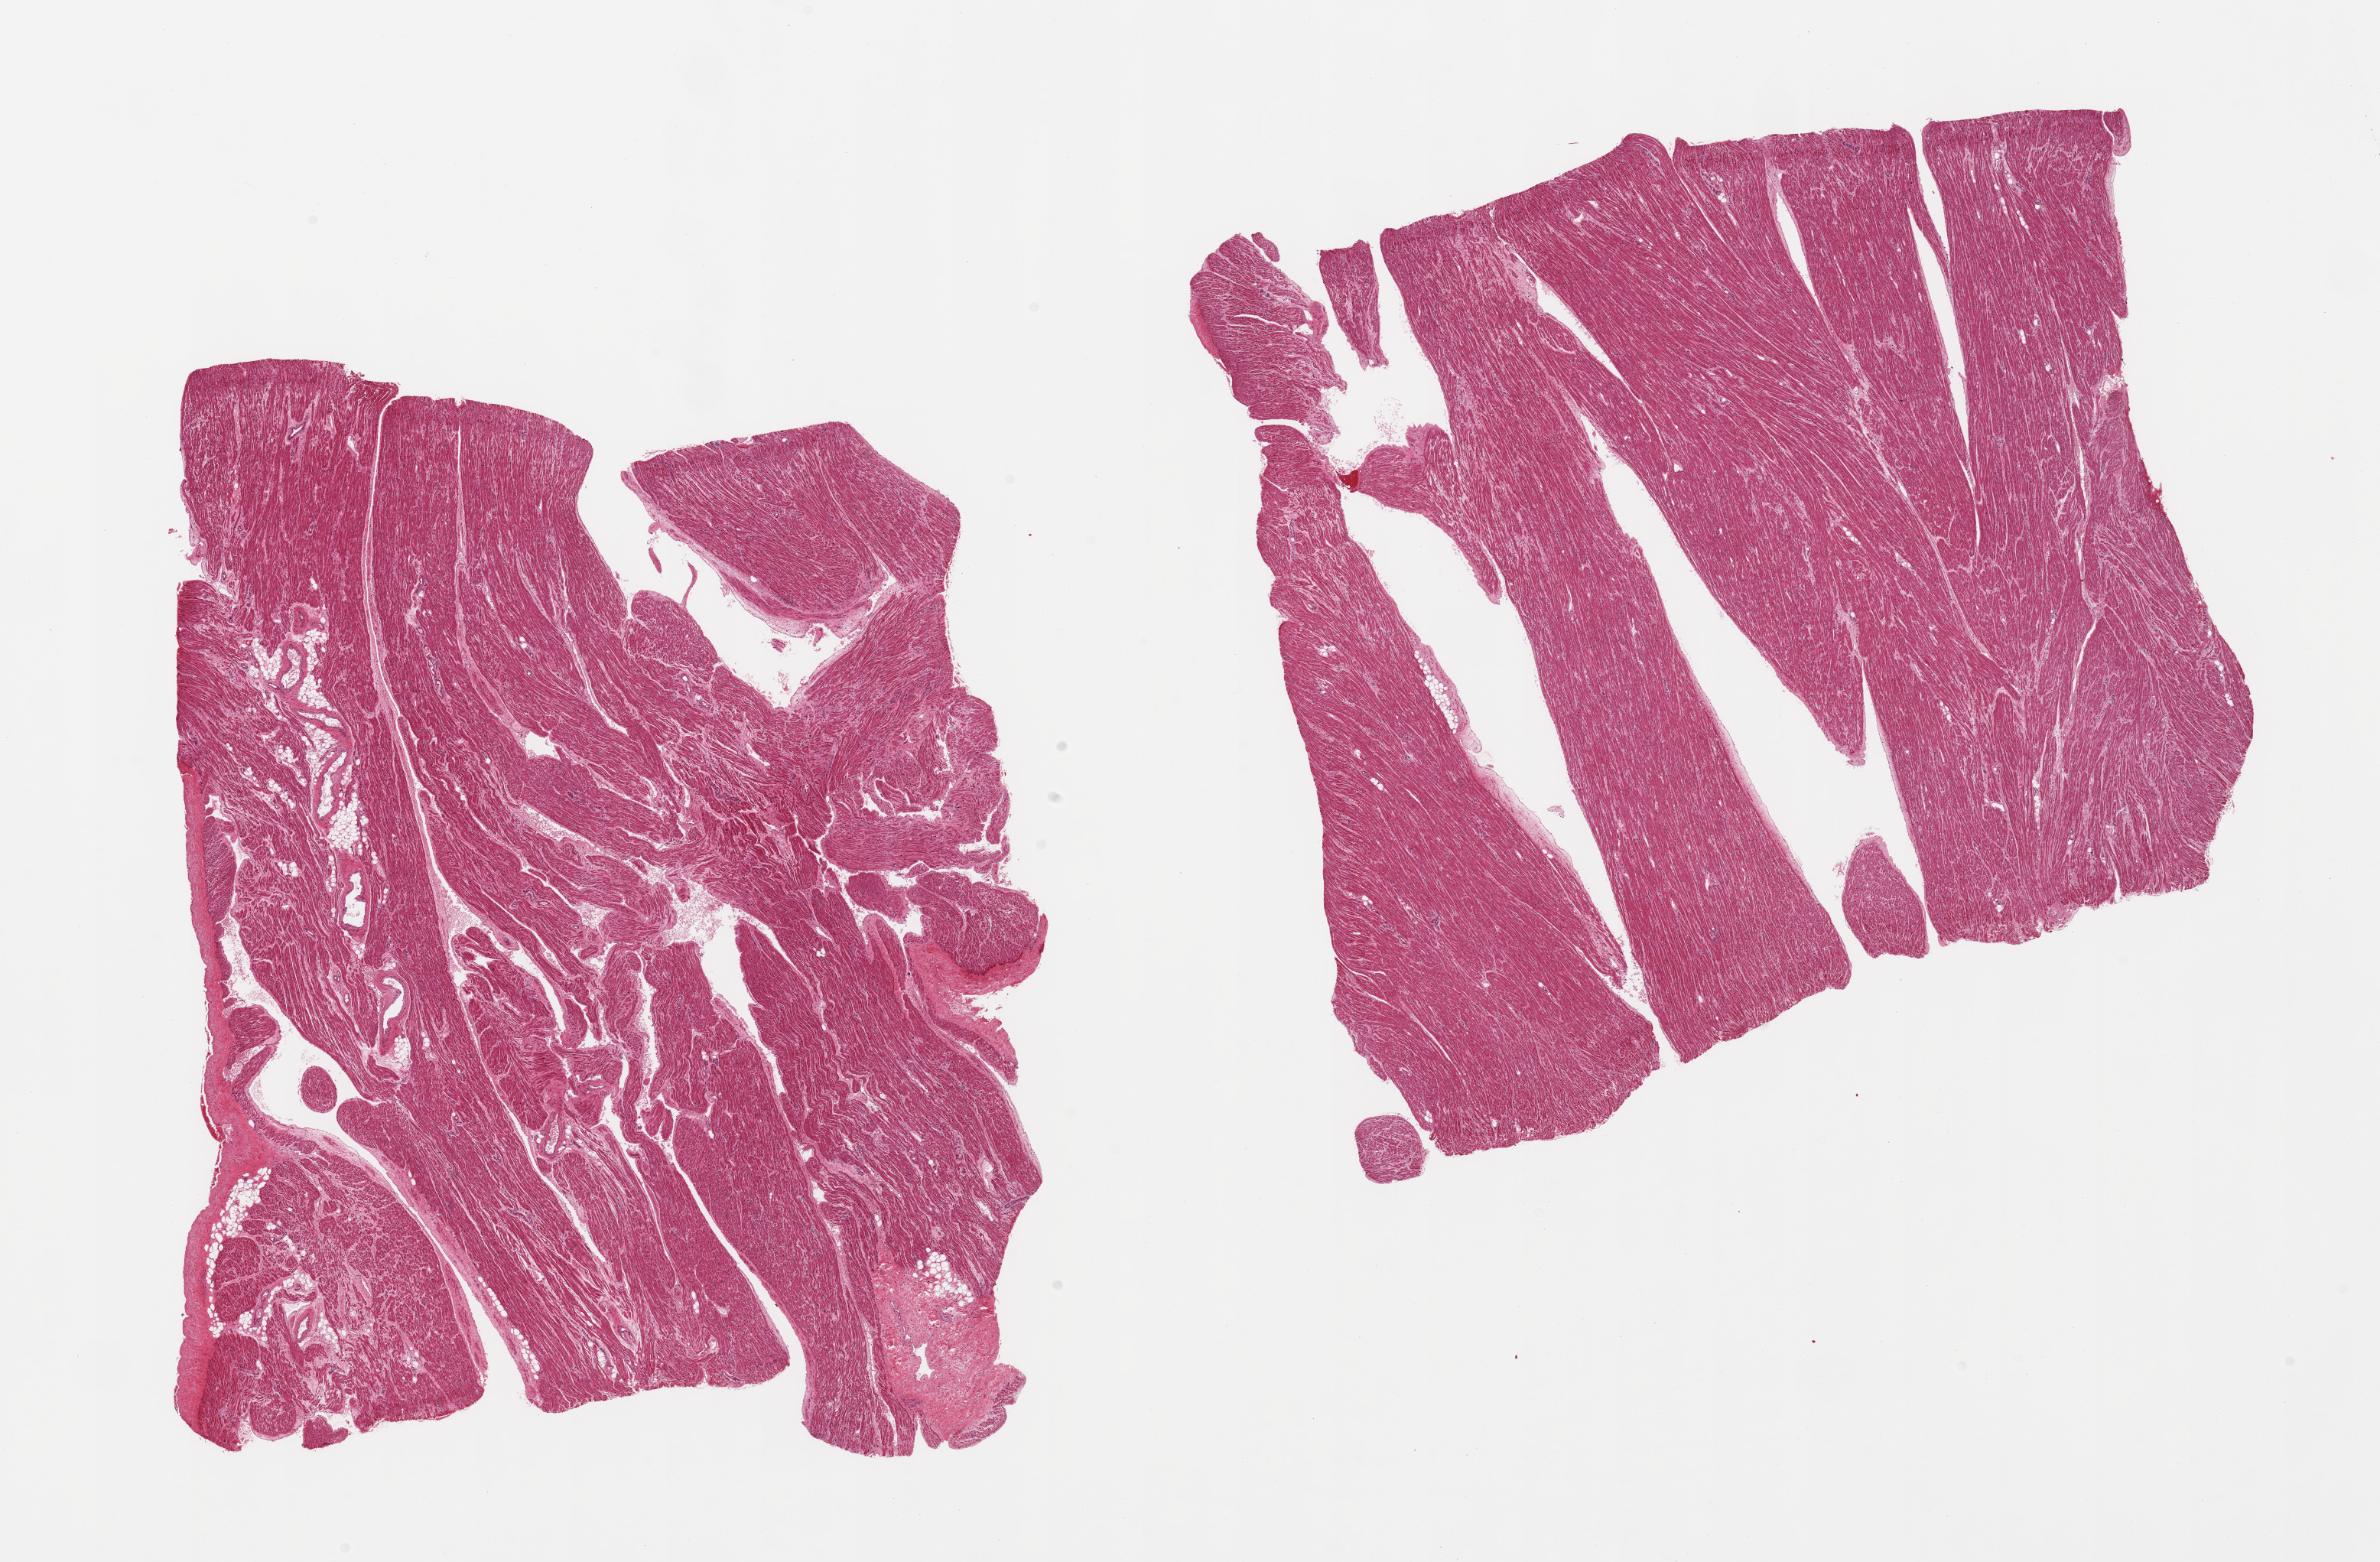
Whole-slide image, H&E stain, brightfield — whole scanned area (about 24.6 x 16.1 mm) shown as a low-resolution overview, PAXgene-fixed, paraffin-embedded tissue, sampled site (target tissue): auricular appendage, donor tissue sample. Male donor.
Review note (as recorded): 2 pieces, no abnormalities.